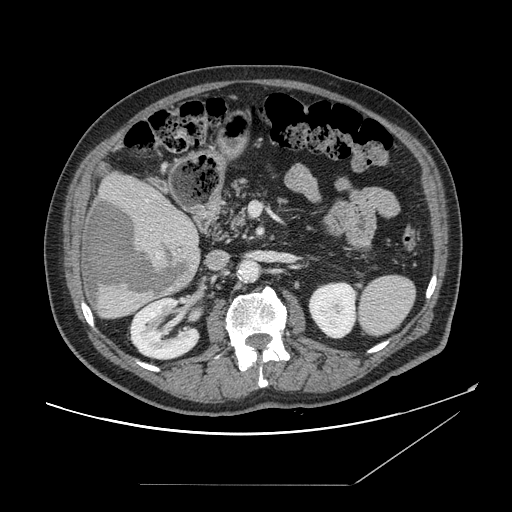
Contrast-enhanced abdominal CT, one axial slice; slice 72 of 166 in the series (ordered by position); 120 kVp; intravenous contrast given; soft-tissue window (W 400 / L 40 HU); 512 × 512 image matrix, field of view 416 × 416 mm. Male patient, age 80 years. From the clinical record (not read from this slice): diagnosis: colorectal cancer liver metastases, imaged before liver resection; multiple liver metastases: no; largest metastasis: 2.2 cm.
Structures marked on this image (expert manual segmentation):
- hepatic veins: bounding box [x1, y1, x2, y2] px = [146, 200, 149, 203]
- liver: [81, 171, 200, 319]
- planned liver remnant (the part of the liver to remain after resection): [105, 171, 186, 220]
- liver metastasis: [85, 199, 189, 307]